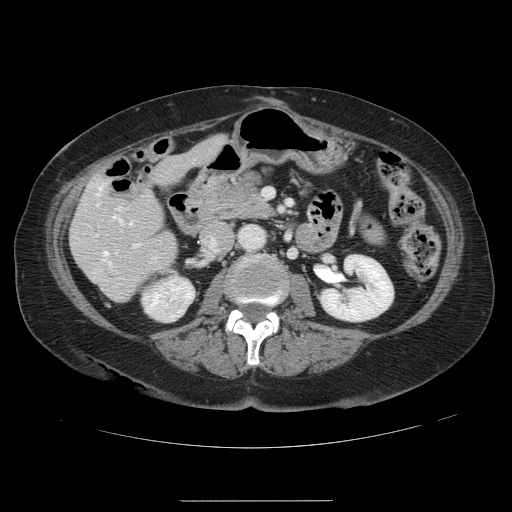
Contrast-enhanced abdominal CT, one axial slice; slice 45 of 141 in the series (ordered by position); 120 kVp; intravenous contrast given; soft-tissue window (W 400 / L 40 HU); 2.5 mm slice thickness; 512 × 512 image matrix. Female patient, age 74 years. Case-level facts recorded for this patient, not image findings: diagnosis: colorectal cancer liver metastases, imaged before liver resection; multiple liver metastases: yes; largest metastasis: 7 cm; disease in both lobes: yes.
Structures marked on this image (outlined manually by an expert reader):
- hepatic veins: bounding box [x1, y1, x2, y2] px = [96, 187, 132, 255]
- liver: [71, 137, 225, 301]
- planned liver remnant (the part of the liver to remain after resection): [71, 137, 225, 289]
- portal vein (with intrahepatic branches): [96, 207, 138, 247]